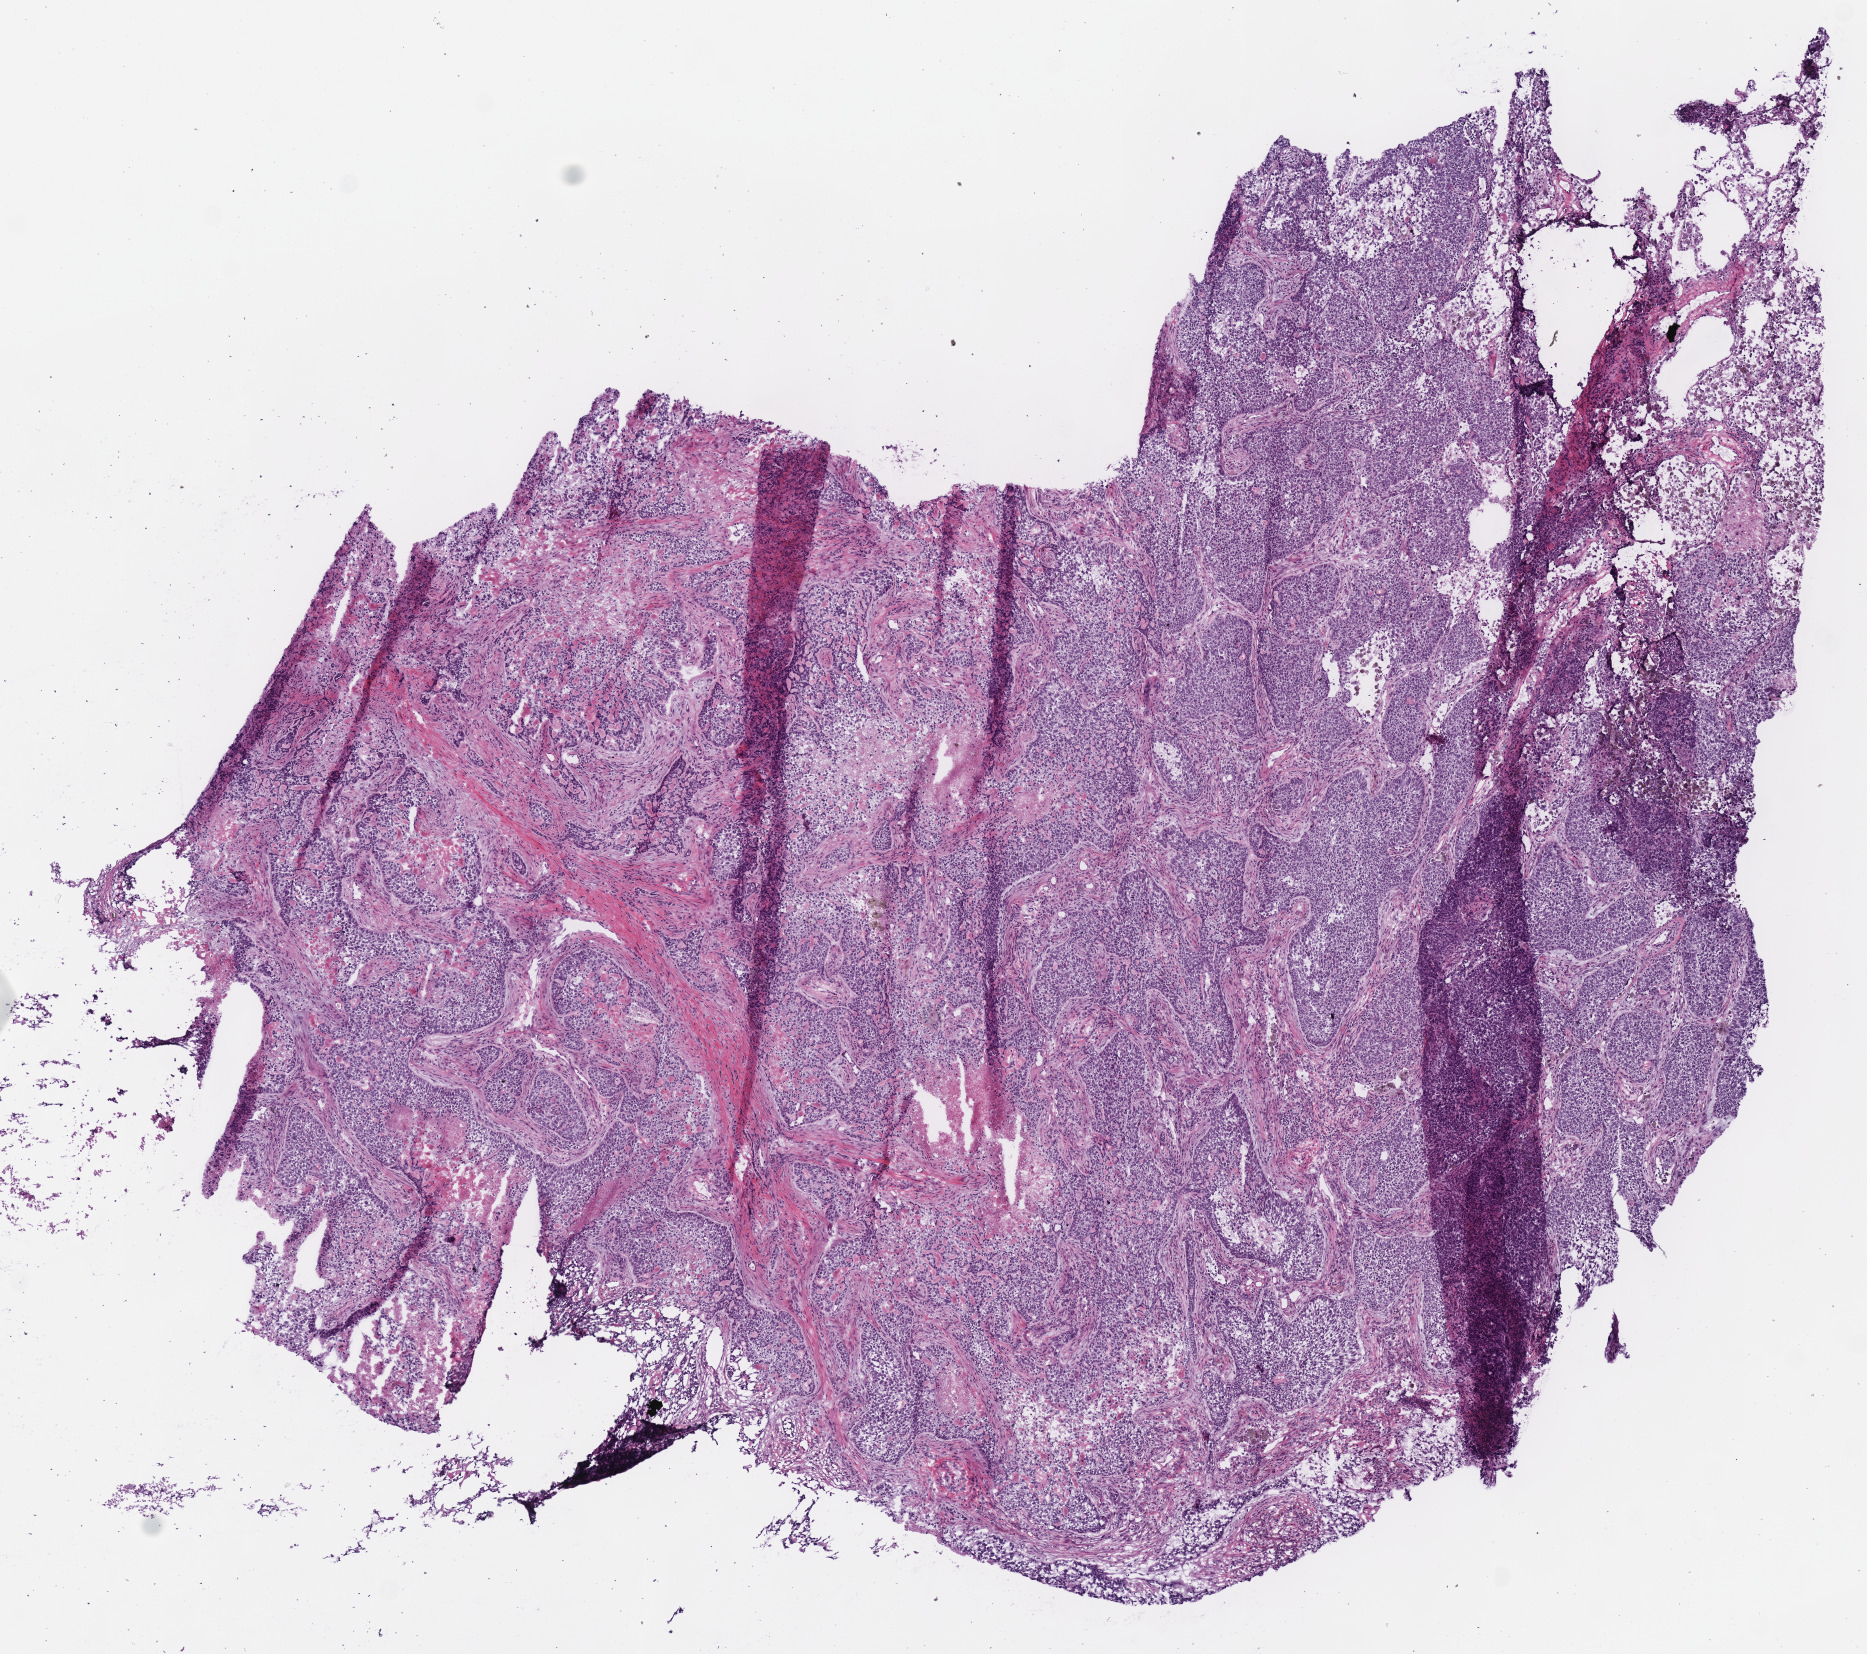
Digitized Hematoxylin and eosin (H&E) stained tissue section (whole slide), shown as a low-resolution overview of the whole scanned area (about 7.3 x 6.5 mm, slide scanned at 40x), frozen section from the bottom of the tissue portion, primary tumour sample from the lung. Male, age 60 years at initial diagnosis. Composition of this section per pathologist review: tumour cells 78%, tumour nuclei 85%, normal cells 2%, stromal cells 10%, necrosis 10%. Inflammatory infiltration, as recorded: lymphocyte infiltration 2%.
AJCC pathologic stage: IB. Diagnosis: Basaloid squamous cell carcinoma (upper lobe, lung).